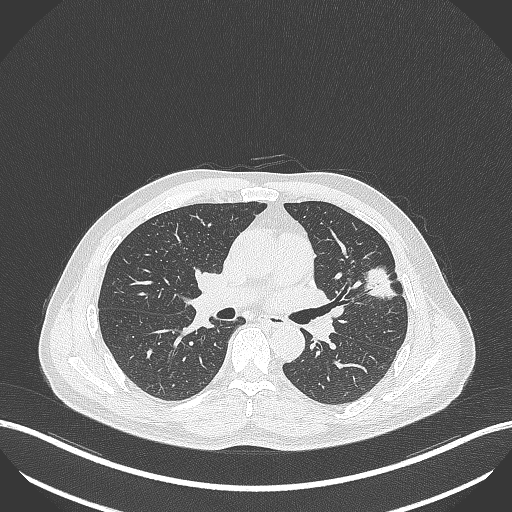
Chest CT, one axial slice. Slice 223 of 418 in the series (ordered by position). 120 kVp. Lung window (W 1500 / L -600 HU). 1 mm slice thickness. 512 × 512 image matrix, field of view 400 × 400 mm. Male patient, age 55 years. Case-level facts recorded for this patient, not image findings: clinical TNM (as recorded): T1c N0 M0.
Annotated regions visible in this slice (rectangle marked by the reading radiologist):
- lung tumour (recorded histology: adenocarcinoma): box from (x=363, y=264) to (x=400, y=303) px